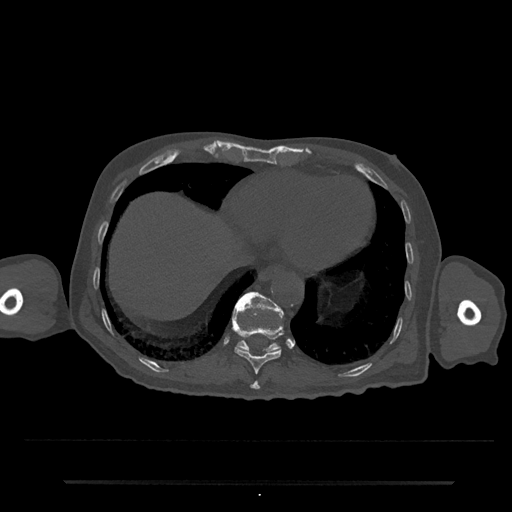
CT including the spine, one axial slice; slice 296 of 797 in the series (ordered by position); reconstruction kernel Br40s/3; bone window (W 1800 / L 400 HU); 512 × 512 image matrix, field of view 427 × 427 mm. Patient: male, 74 years. Case-level facts recorded for this patient, not image findings: primary cancer: prostate.
Structures marked on this image (semi-automatic segmentation, software-assisted and operator-edited):
- T10 vertebra: bounding box (x1, y1, x2, y2) in pixels: (232, 315, 284, 374)
- T11 vertebra: (233, 292, 283, 353)
- T9 vertebra: (250, 381, 260, 390)